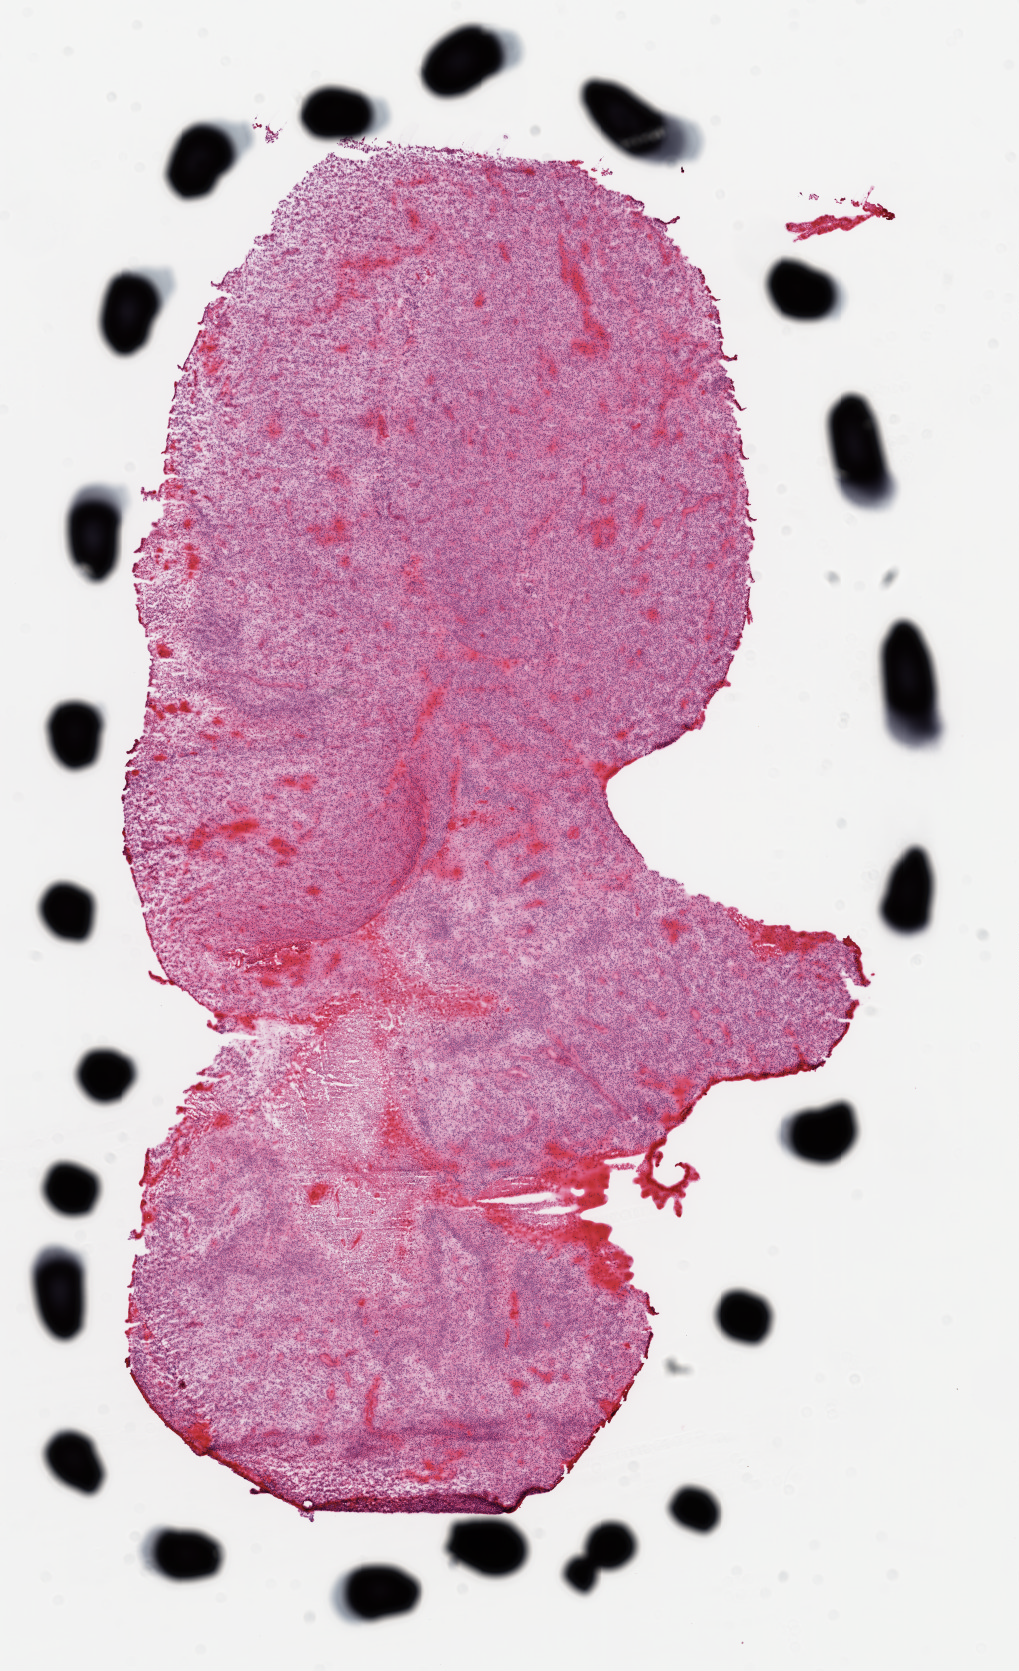
H&E-stained whole-slide image — shown as a low-resolution overview of the whole scanned area (about 8.2 x 13.5 mm, acquisition: 20x scan); frozen section; brain, primary tumour sample. Male patient; age at initial diagnosis 65 years. Composition of this section per pathologist review: tumour cells 75%, tumour nuclei 95%, necrosis 25%. Infiltration values recorded for this section: neutrophil infiltration 100%.
* diagnosis: Glioblastoma